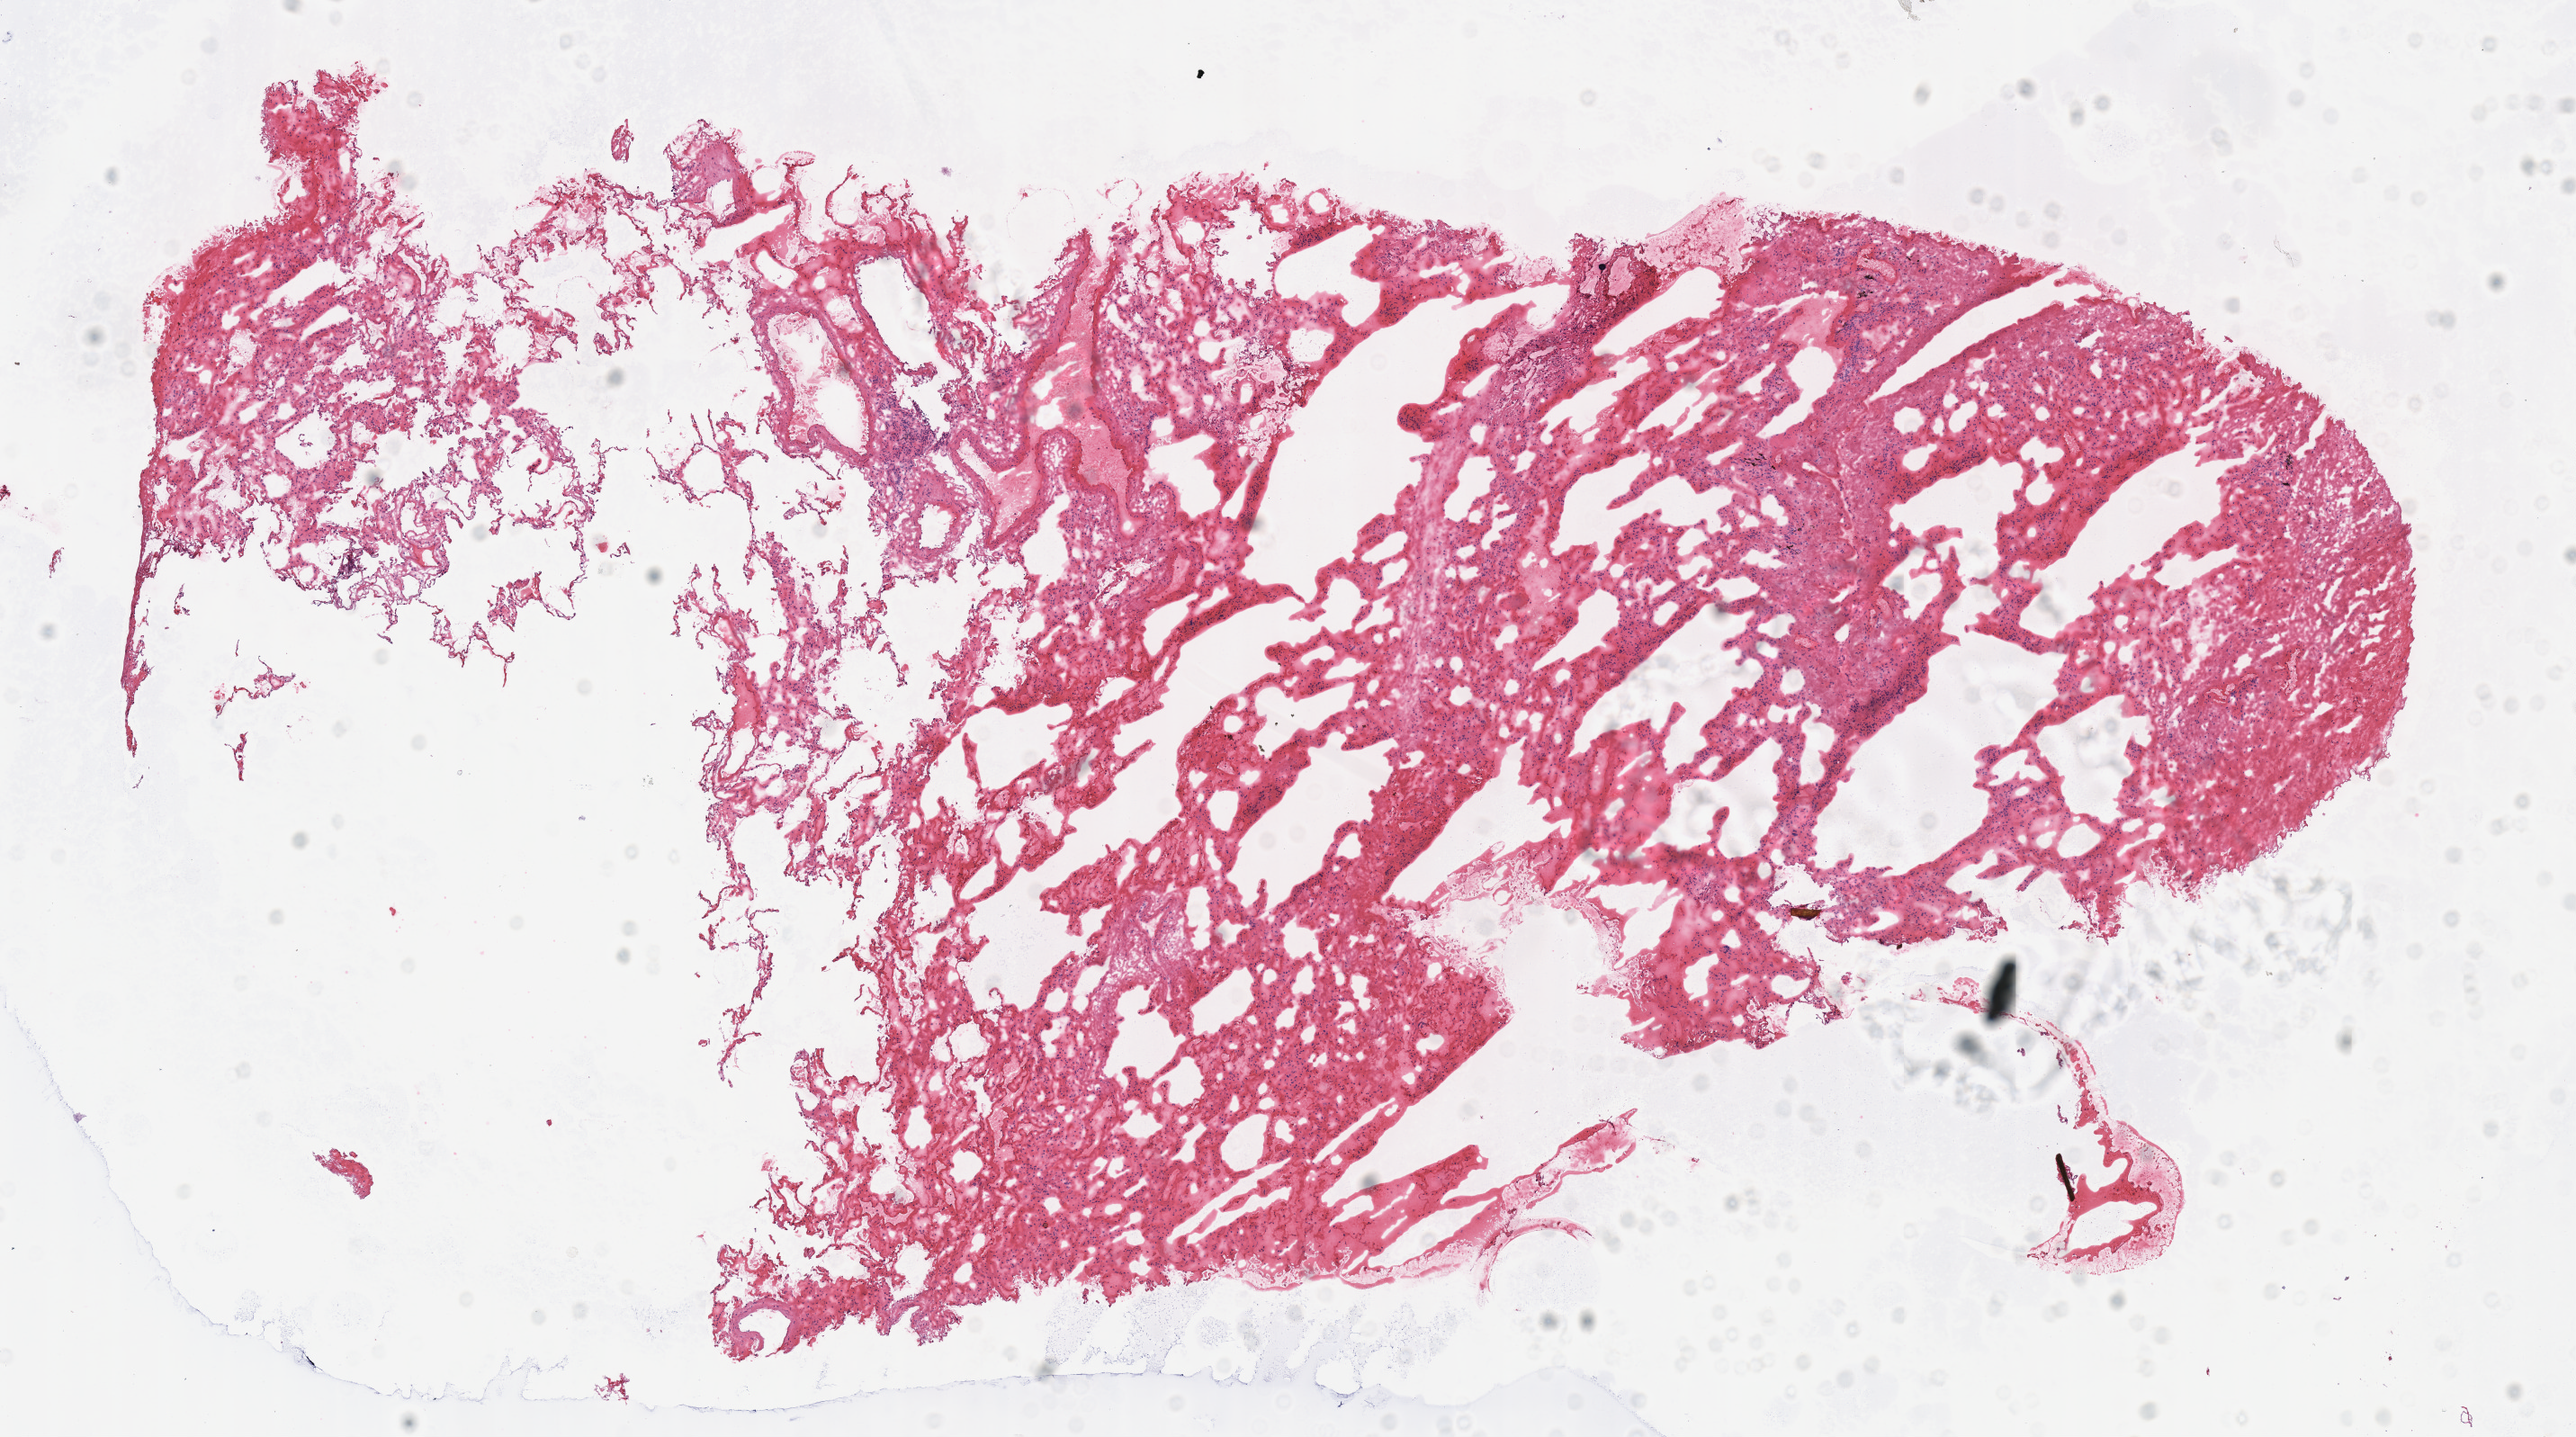
Whole-slide histology image, Hematoxylin and eosin (H&E) stained, shown as a low-resolution overview of the whole scanned area (about 11.3 x 6.3 mm, from a 40x scan); frozen section from the top of the tissue portion; solid tissue normal (non-tumour tissue) sample from the lung. Patient: female, age at initial diagnosis 65 years. Inflammatory infiltration, as recorded: lymphocyte infiltration 5%, monocyte infiltration 0%, neutrophil infiltration 0%.
This section: solid tissue normal sample (biorepository sample class). Patient diagnosis: Adenocarcinoma, NOS (upper lobe, lung).